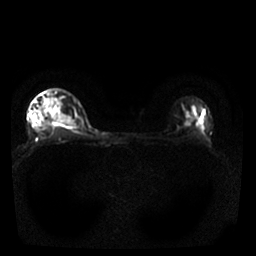
Breast MRI, one axial slice; slice 21 of 25 in the series (ordered by position); diffusion-weighted series; image 2 of 4 stored at this slice position (different b-values; order by instance number); 1.5 T; 256 × 256 image matrix, field of view 310 × 310 mm. Female patient.
Outlined on this slice (outlined manually by an expert reader):
- tumour on diffusion-weighted imaging: bounding box [x1, y1, x2, y2] px = [64, 115, 73, 126]